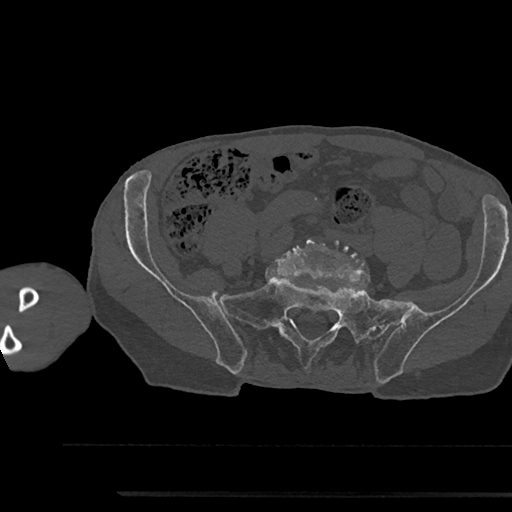
CT including the spine, one axial slice; position 306 of 797 along the scan axis; bone window (W 1800 / L 400 HU); 512 × 512 image matrix. Patient: male, 79 years. From the clinical record (not read from this slice): primary cancer: prostate.
Structures marked on this image (semi-automatically segmented with operator editing):
- L5 vertebra: box from (x=276, y=235) to (x=370, y=283) px